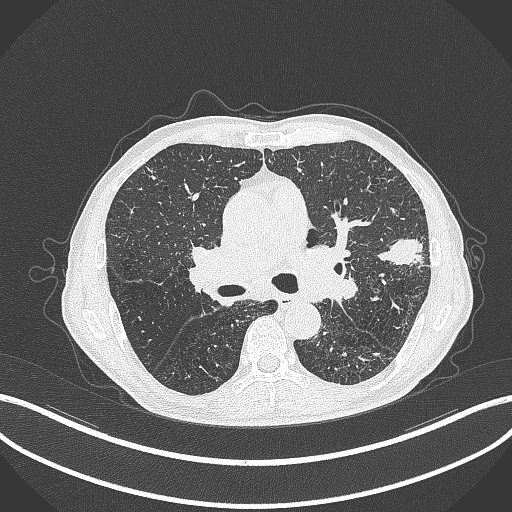
Chest CT, one axial slice; position 250 of 463 along the scan axis; reconstruction kernel B70f; 120 kVp; lung window (W 1500 / L -600 HU); 1 mm slice thickness; 512 × 512 image matrix. Male patient, age 74 years. Case-level facts recorded for this patient, not image findings: clinical TNM (as recorded): T2a N1 M0.
Annotated regions visible in this slice (rectangle marked by the reading radiologist):
- lung tumour (recorded histology: adenocarcinoma): box from (x=374, y=237) to (x=424, y=273) px